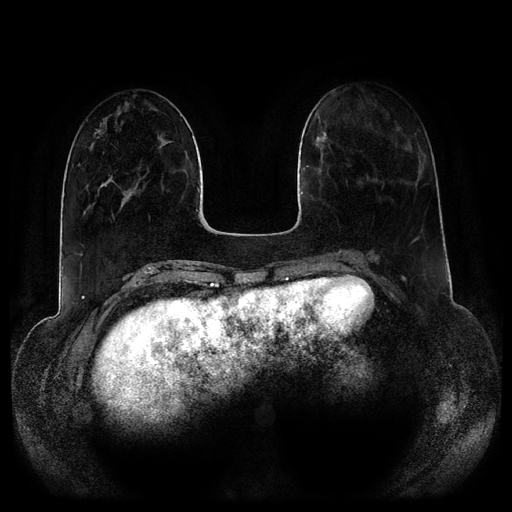
Breast MRI (dynamic contrast-enhanced, multi-phase), one axial slice. Slice 36 of 116 in the series (ordered by position). Dynamic contrast-enhanced series, time point 2 of 5 at this slice position (early post-contrast). 1.5 T. TE 2.5 ms, TR 5.2 ms. 2 mm slice thickness. 512 × 512 image matrix, field of view 390 × 390 mm. Patient: female, 34 years.
Outlined on this slice (semi-automatic segmentation, software-assisted and operator-edited):
- breast lesion (labelled benign in the annotation): bounding box [x1, y1, x2, y2] px = [313, 131, 330, 150]